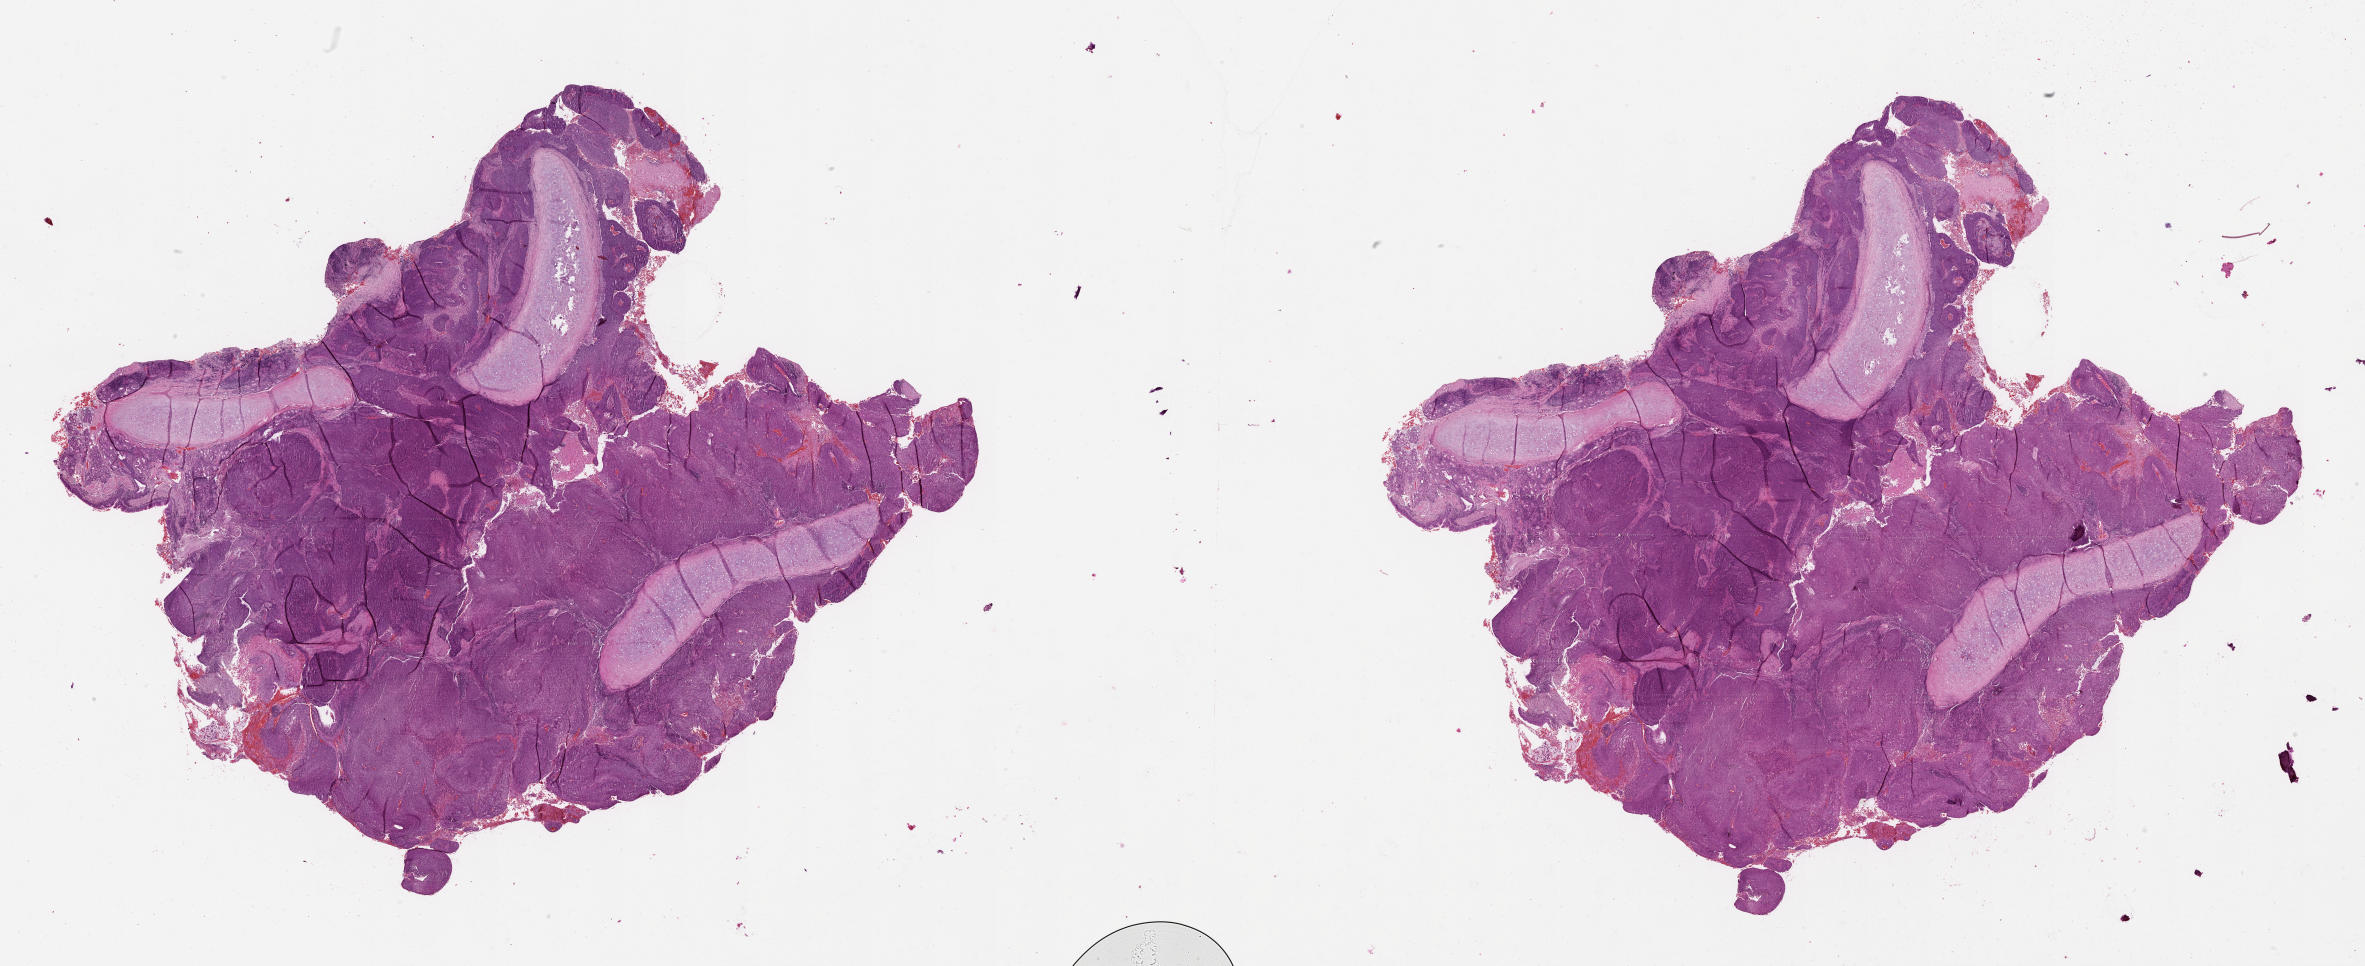
Digitized H&E-stained tissue section (whole slide) — shown as a low-resolution overview of the whole scanned area (about 38.1 x 15.6 mm, from a 20x scan); lung, tumour tissue. 71-year-old male patient.
Patient diagnosis (cohort enrolment): squamous cell carcinoma (lung).